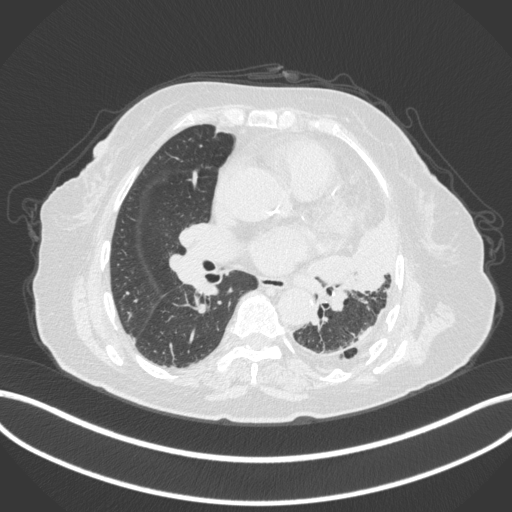
Chest CT, one axial slice; slice 187 of 399 in the series (ordered by position); reconstruction kernel B31f; lung window (W 1500 / L -600 HU); 1 mm slice thickness; 512 × 512 image matrix. Female patient, age 75 years. From the clinical record (not read from this slice): clinical TNM (as recorded): T3 N3 M1.
Outlined on this slice (bounding box drawn by a radiologist):
- lung tumour (recorded histology: adenocarcinoma): bounding box [x1, y1, x2, y2] px = [305, 219, 407, 303]